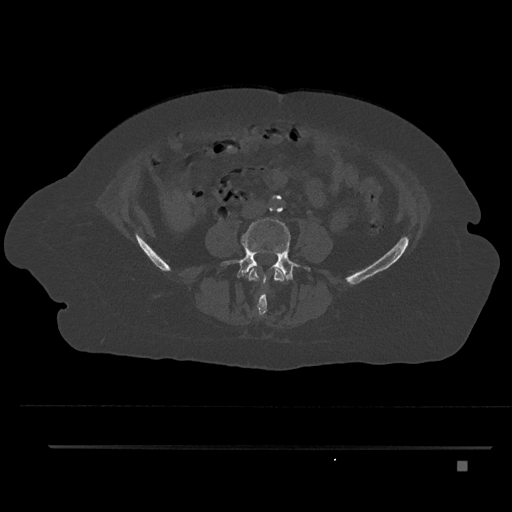
CT including the spine, one axial slice; position 93 of 797 along the scan axis; bone window (W 1800 / L 400 HU); 0.5 mm slice thickness; 512 × 512 image matrix. Female patient, age 76 years. From the clinical record (not read from this slice): primary cancer: lung; vertebrae with lytic lesions (as recorded): T11, L3.
Annotated regions visible in this slice (semi-automatically segmented with operator editing):
- L3 vertebra: bounding box (x1, y1, x2, y2) in pixels: (248, 267, 285, 315)
- L4 vertebra: (221, 217, 310, 297)